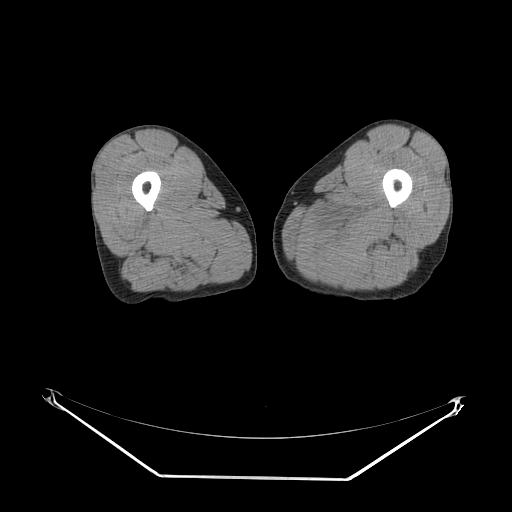
CT of an extremity soft-tissue mass (from a PET/CT study), one axial slice; slice 12 of 267 in the series (ordered by position); reconstruction kernel SOFT; 140 kVp; soft-tissue window (W 400 / L 40 HU); 3.75 mm slice thickness; 512 × 512 image matrix, field of view 500 × 500 mm. Male patient. Case-level facts recorded for this patient, not image findings: histological type: pleiomorphic liposarcoma; grade: high; site of the primary tumour: left thigh.
Outlined on this slice (expert contour drawn on MRI and transferred to this co-registered scan by the dataset authors):
- gross tumour volume including surrounding oedema: bounding box (x1, y1, x2, y2) in pixels: (320, 203, 373, 270)